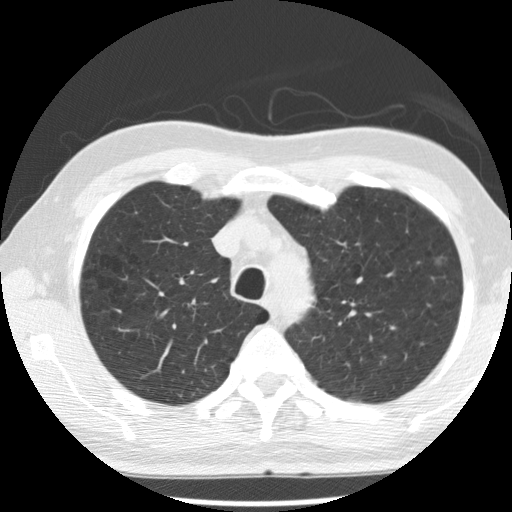
Low-dose screening chest CT, axial slice, first (baseline) screen, lung window (W 1500 / L -600 HU), 2.5 mm slice thickness. Male, age 68 years at enrolment. Current smoker at enrolment.
Expert-annotated lung lesion, bounding box (x1, y1, x2, y2) in pixels: (426, 249, 462, 281). Screening reader's record for this exam (one nodule recorded; not confirmed to be the boxed lesion): non-calcified nodule or mass ≥4 mm, left upper lobe, 5 × 5 mm, poorly defined margins, ground glass attenuation. Lung cancer was diagnosed 648 days after this screen: bronchiolo-alveolar adenocarcinoma, NOS, left upper lobe, moderately differentiated (G2), stage IA (AJCC 6th edition), 17 mm at pathology.